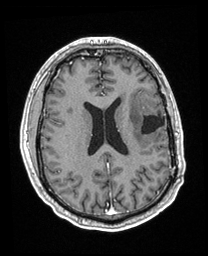
Brain MRI from a brain-tumour surgery series, one axial slice. Slice 90 of 208 in the series (ordered by position). T1-weighted post-contrast. 1 mm slice thickness. 208 × 256 image matrix, field of view 211 × 260 mm. Case-level facts recorded for this patient, not image findings: histopathology: Astrocytoma; WHO grade: 3; IDH mutation: yes.
Structures marked on this image (expert manual segmentation):
- previous resection cavity: bounding box (x1, y1, x2, y2) in pixels: (141, 113, 165, 134)